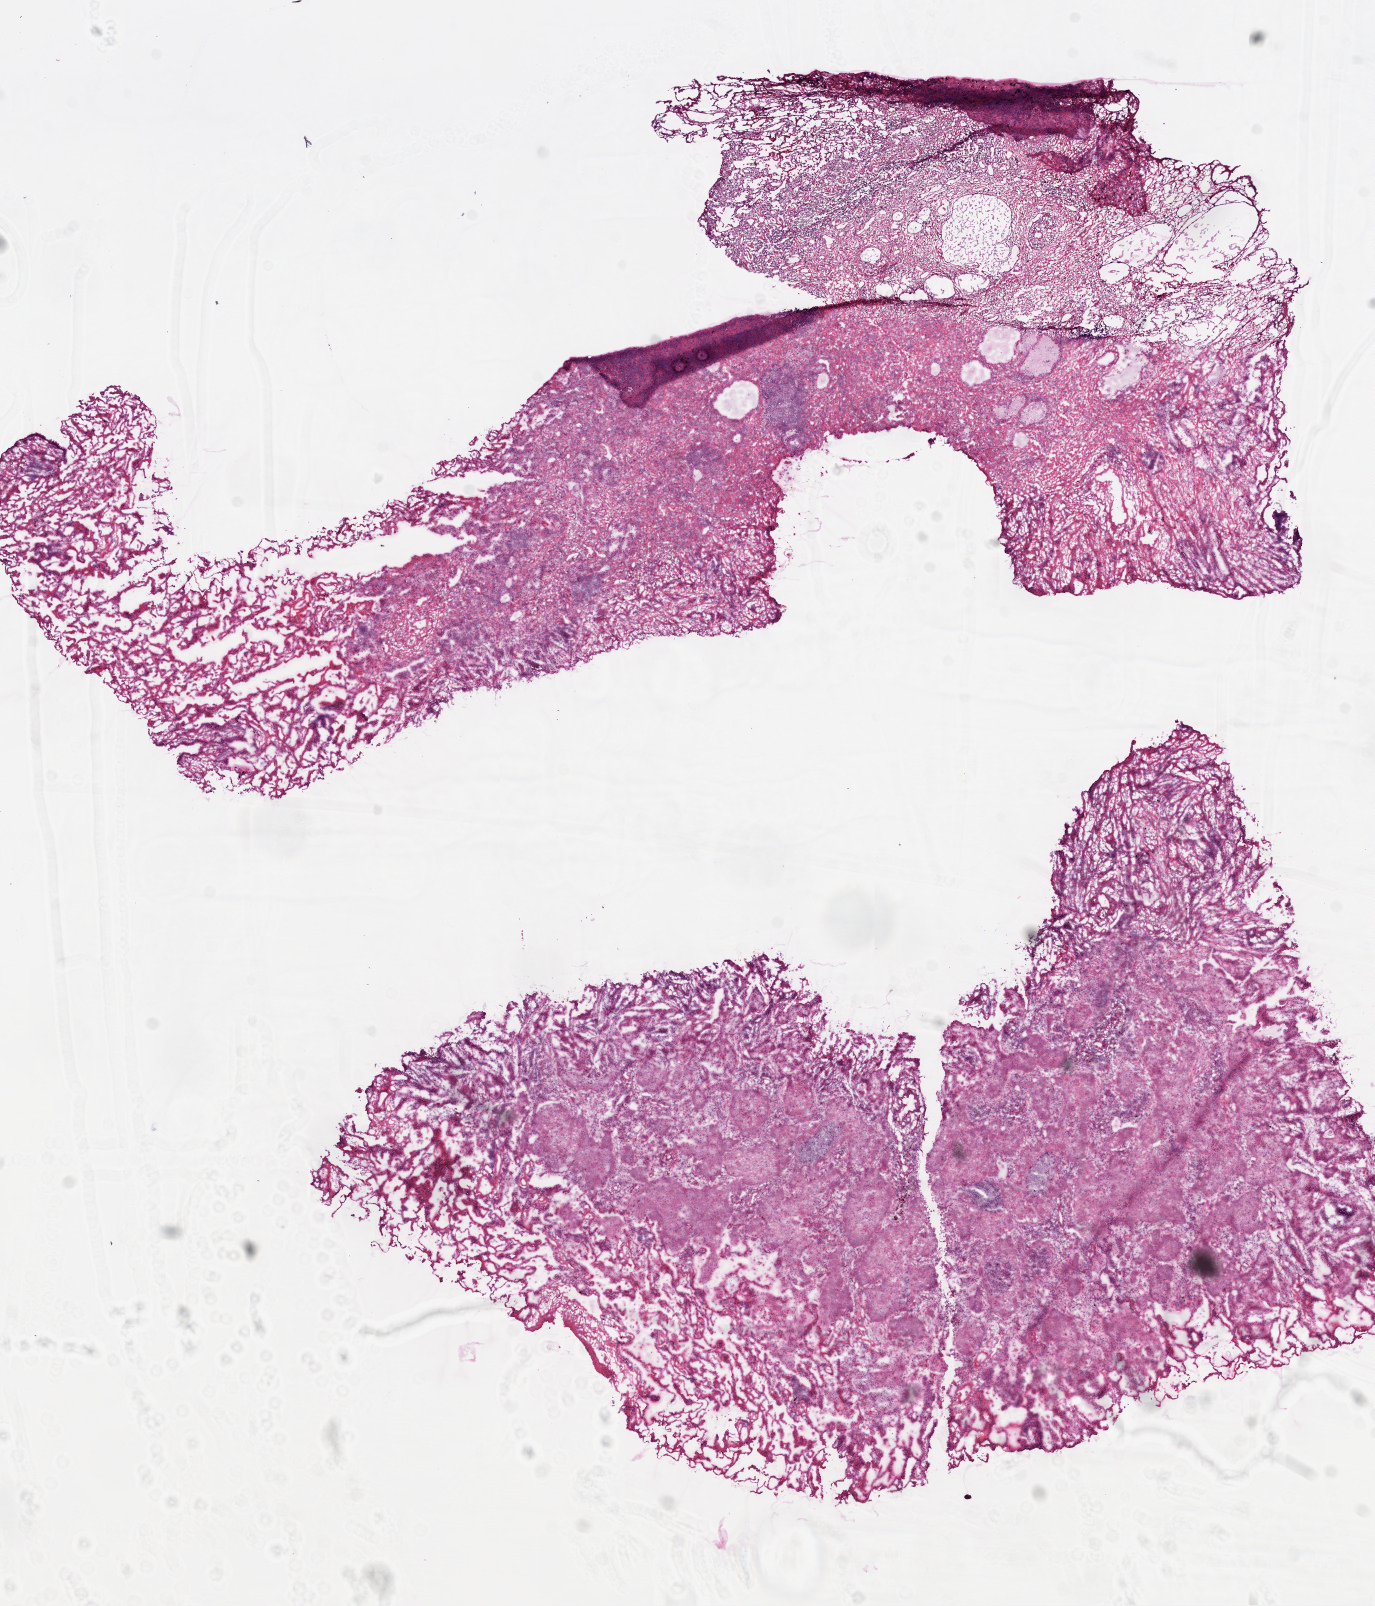
Whole-slide histology image, H&E-stained, whole scanned area (about 11.0 x 12.9 mm) shown as a low-resolution overview. Frozen section from the top of the tissue portion. Sample: primary tumour, lung. Female, age 80 years at initial diagnosis.
Histologic diagnosis: Squamous cell carcinoma, NOS (upper lobe, lung).